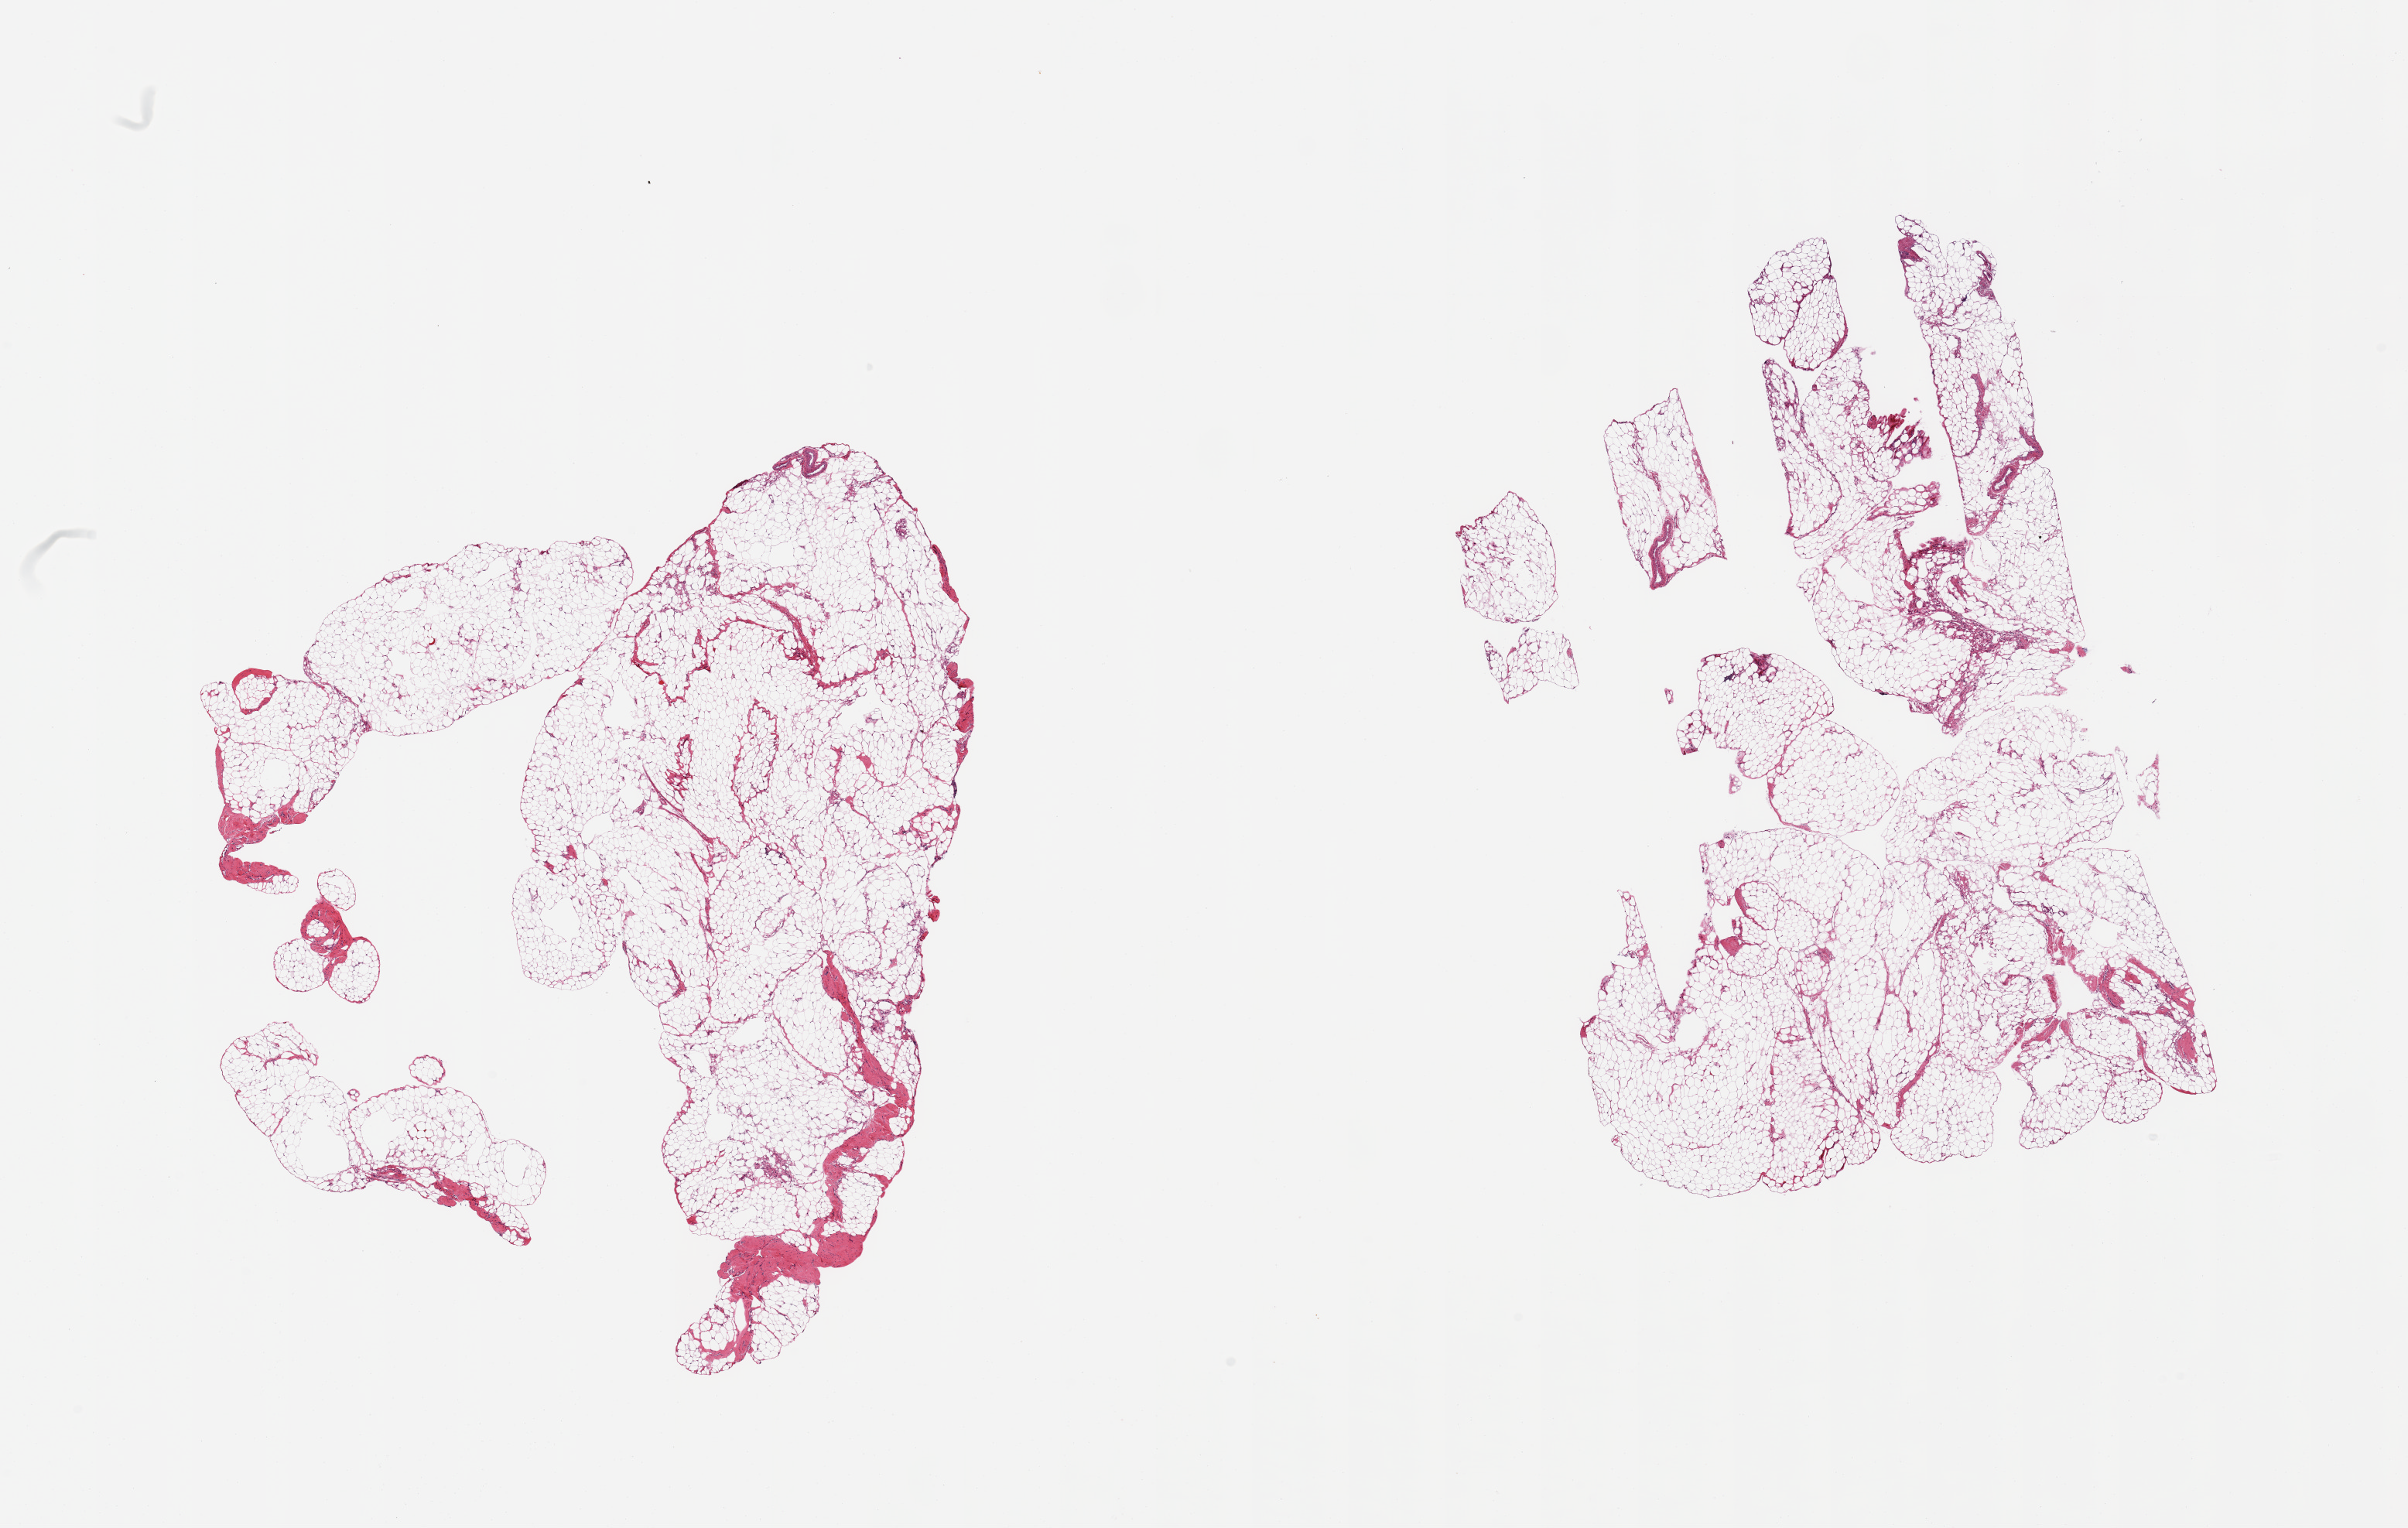
Haematoxylin and eosin whole-slide image, brightfield, shown as a low-resolution overview of the whole scanned area (about 24.6 x 15.6 mm, from a 20x scan), PAXgene-fixed, paraffin-embedded tissue, sampled site (target tissue): omentum, donor tissue sample. Donor: male.
- reviewer comment on this tissue sample: 2 pieces; 5% fibrous content